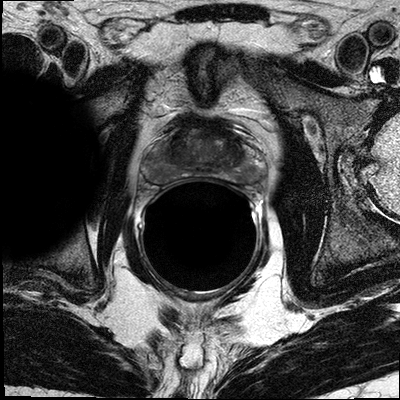
Prostate MRI examination; 3 images, each a single mid-volume slice chosen by position (not for content). Treatment context recorded for this patient: Surgery.
Image 1: axial T2-weighted image, series "T2W_TSE_AX", slice 17 of 32, 3 mm slice thickness.
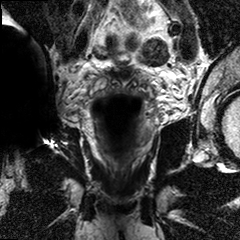
Image 2: coronal T2-weighted image, slice 13 of 24, 3 mm slice thickness.
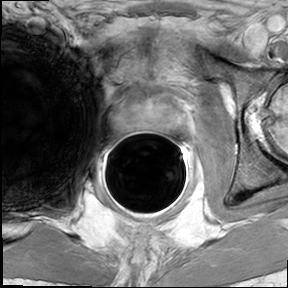
Image 3: axial dynamic contrast-enhanced (DCE) T1-weighted image, slice 17 of 32, dynamic phase 5 of 8, 6 mm slice thickness.
Report of this MRI examination:
Normal prostate anatomy is preserved. Imaging findings suggestive for chronic prostatitis and BPH. The prostate shows on both sides within the posterior lateral peripheral zones (mid third) smaller areas of signal alteration in geographic configuration and abnormal enhancement on the dynamic images. The largest area on the left posterior lateral zone measures 9 x 7 mm on the right 5 x 6 mm. The prostate pseudo capsule on either side are normal. There is no evidence of capsular infiltration, or extra glandular extension on either side. There is no evidence of seminal vesicle infiltration. There is no evidence of pelvic lymphadenopathy. IMPRESSION: Imaging findings suggestive for bilateral prostate cancer with smaller nodules on both sides. No evidence of extra glandular extension or neurovascular bundles involvement. Based on these imaging results nerve sparing would be possible on both sides. No Seminal vesicles infiltration; no pelvic lymphadenopathy. Chronic prostatitis. BPH.

Prostate biopsy pathology (as recorded):
specimen consists of multiple tan core biopsies measuring in length from 0.2 cm to 2.2 cm and 0.1 cm in diameter each. The specimen is submitted in toto in seven cassettes as follows: 1 right PZ, 2 right PZ/TZ, 3 right apex, 4 left PZ, 5 left PZ/TZ, 6 left apex, 7 floaters. PROSTATE BIOPSIES: 1. RIGHT PZ:
PROSTATIC ADENOCARCINOMA, GLEASON SCORE 3+4=7/10, INVOLVING ONE CORE, ABOUT 30% OF TISSUE REPRESENTED. 2. RIGHT PZ/TZ: PROSTATIC ADENOCARCINOMA, GLEASON SCORE 3+4=7/10, INVOLVING THREE CORES, ABOUT 20% OF TISSUE REPRESENTED. 3. RIGHT APEX: PROSTATIC ADENOCARCINOMA, GLEASON SCORE 3+4=7/10, INVOLVING ONE CORE, ABOUT 30% OF TISSUE REPRESENTED. 4. LEFT PZ: PROSTATIC TISSUE WITH MICROSCOPIC FOCUS OF ATYPICAL SMALL ACINAR PROLIFERATION. 5. LEFT PZ/TZ: PROSTATIC ADENOCARCINOMA, GLEASON SCORE 3+3=6/10, INVOLVING TWO CORES, ABOUT 10% OF TISSUE REPRESENTED. 6. LEFT APEX: FIBROCONNECTIVE TISSUE. NO TUMOR IDENTIFIED. 7. FLOATERS: PROSTATIC TISSUE WITH MICROSCOPIC FOCUS OF ATYPICAL SMALL ACINAR PROLIFERATION.

Prostatectomy specimen pathology (as recorded; the surgery followed this MRI):
Gross Description
A. "Left Pelvic Lymph Node Packet", B. "Right Pelvic Lymph Node Packet" and C. "Prostate and Seminal Vesicles". Specimen A consists of a single fragment of adipose tissue measuring 5x2.5x0.5 cm. One lymph node is identified measuring 2.5x1x0.3 cm. The lymph node is submitted in a single cassette labeled A. Specimen B consists of a single fragment of adipose tissue measuring 3x2.5x0.5 cm. Two lymph nodes are identified measuring 0.5x0.3x0.2 cm and 2.5x1x0.3 cm. The lymph nodes are submitted in two cassettes labeled B1 and B2. Specimen C consists of a prostatectomy specimen weighing 34.3 grams and measuring 5x3x3 cm. The seminal vesicles measures 4x1 cm each. The vas deferens measures 5x0.2 cm each. The right side of the prostate is inked black and the left side is inked blue. The prostate is serially sectioned from the apex to the bladder neck revealing granularity cut surface. The specimen is submitted in cassettes as follows: C1 shaved apex margin, C2 shaved bladder neck margin, C3 thru C6 anterior right prostate, serially sectioned from the apex to the base, C7 thru C13 posterior right prostate, serially sectioned from the apex to the base, C14 thru C17 anterior left prostate, serially sectioned from the apex to the base, C18 thru C23 posterior left prostate, serially sectioned from the apex to the base, C24 right seminal vesicle and vas deferens, C25 left seminal vesicle and vas deferens.
Final Diagnosis A.LEFT PELVIC LYMPH NODE PACKET: ONE (1) REACTIVE LYMPH NODE, NO TUMOR IDENTIFIED. B.RIGHT PELVIC LYMPH NODE PACKET: TWO (2) REACTIVE LYMPH NODES, NO TUMOR IDENTIFIED C.PROSTATE AND SEMINAL VESICLES: Procedure: Radical prostatectomy Prostate Size: Weight: 34.3gms Size: 5x3x3cm Lymph Node Sampling: Pelvic lymph node dissection Histologic Type: Adenocarcinoma (acinar, not otherwise specified) Histologic Grade: Primary Pattern Grade 3 Secondary Pattern Grade 4 Total Gleason Score: 7 Tumor Quantitation: Proportion (percentage) of prostate involved by tumor: 20%
Extraprostatic Extension: Not identified Seminal Vesicle Invasion: Not identified Margins: Margins uninvolved by invasive carcinoma Treatment Effect on Carcinoma: Not identified Lymph-Vascular Invasion: Not identified Perineural Invasion: Present Pathologic Staging (pTNM) Primary Tumor (pT) pT2c:Bilateral disease Regional Lymph Nodes (pN) pN0:No regional lymph node metastasis Specify:Number examined: 3 Number involved: 0 Distant Metastasis (pM) Not applicable Additional Pathologic Findings: High grade prostatic intraepithelial neoplasia (PIN), and chronic inflammation AJCC Pathologic Stage: (pT2c, pN0) Clinical diagnosis and History: PSA 6.6